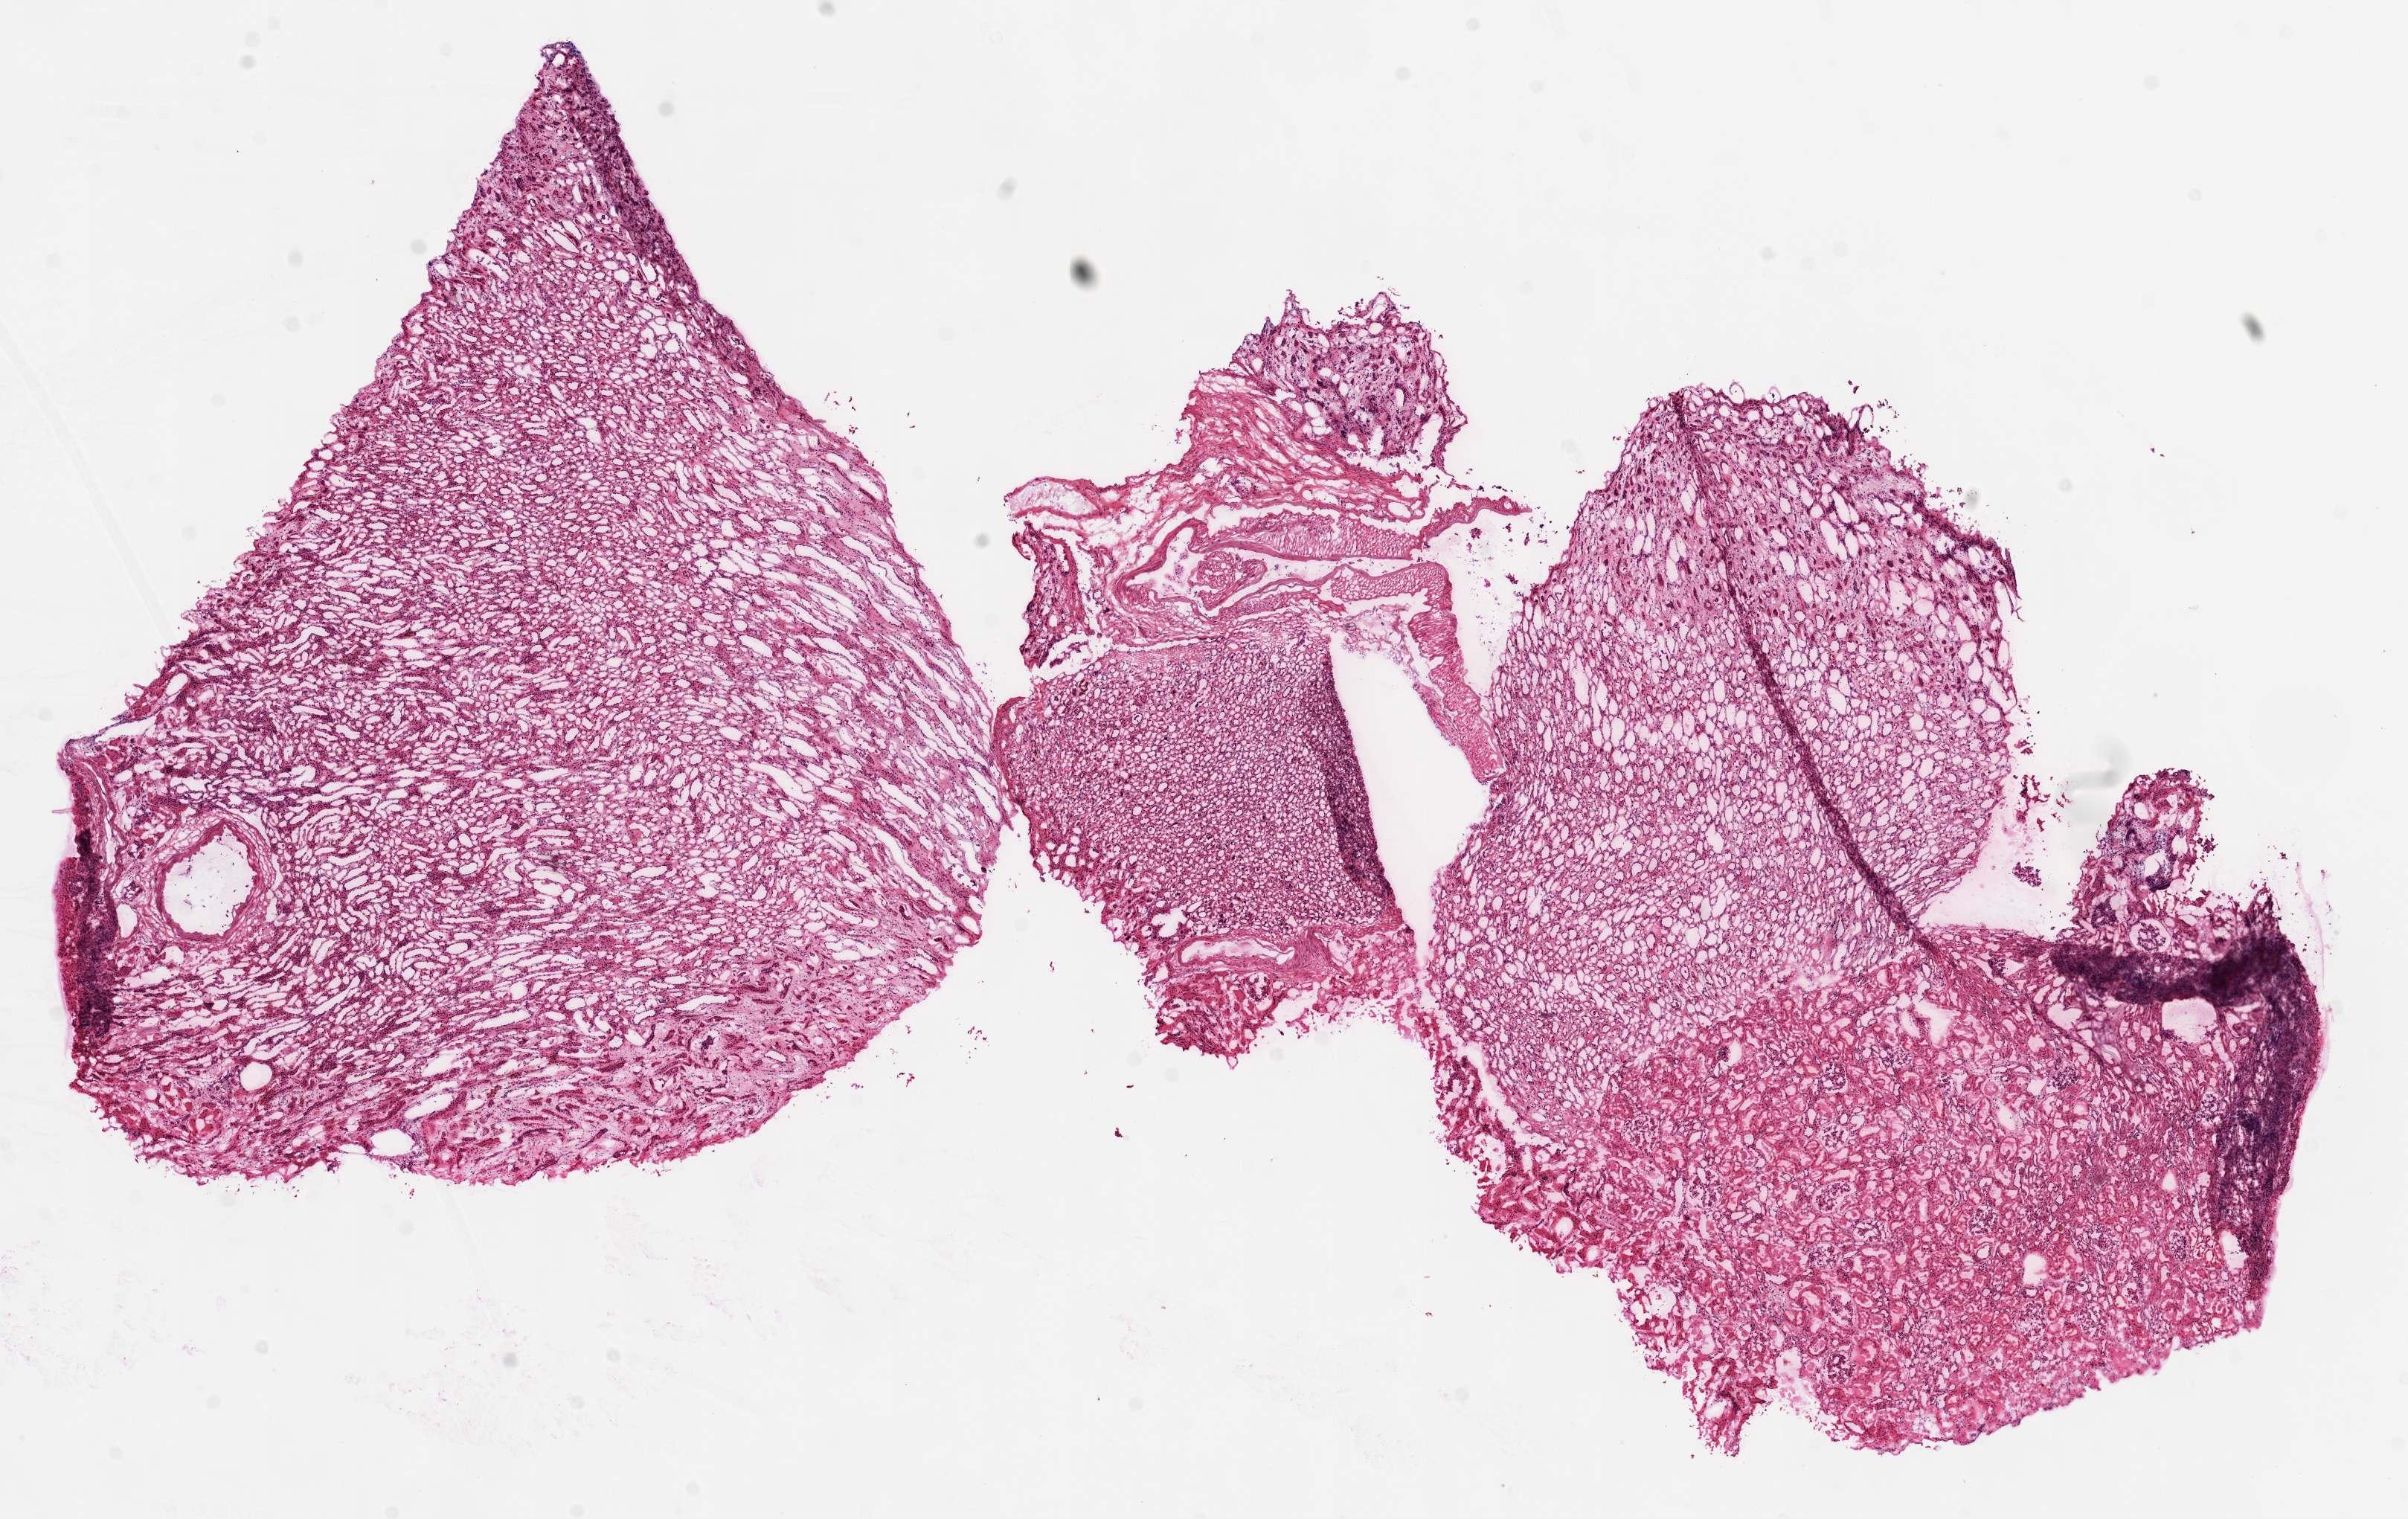
Digitized H&E tissue section (whole slide), shown as a low-resolution overview of the whole scanned area (about 13.1 x 8.2 mm, from a 20x scan). Frozen section from the top of the tissue portion. Kidney, solid tissue normal (non-tumour tissue) sample. Female patient; age at initial diagnosis 59 years.
This section: solid tissue normal sample (biorepository sample class). Patient diagnosis: Clear cell adenocarcinoma, NOS.